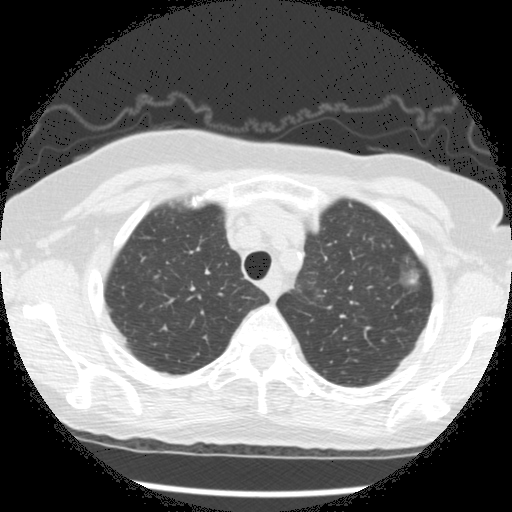
Axial slice from a low-dose chest CT screening exam. Second screening round (one year after baseline). Lung window (W 1500 / L -600 HU). 2.5 mm slice thickness. Slice 38 of 266 in the series. 512 × 512 image matrix, field of view 320 × 320 mm. Female participant, aged 73 years at enrolment. Former smoker at enrolment.
Expert-annotated lung lesion, bounding box <390,247,433,290> (left, top, right, bottom; pixels). The screening reader recorded 3 non-calcified nodules or masses ≥4 mm on this exam (left upper lobe, left upper lobe, left upper lobe); which of them this box marks is not recorded. Official screen result: positive, change unspecified: nodule(s) >= 4 mm or enlarging nodule(s), mass(es), or other non-specific abnormalities suspicious for lung cancer. Lung cancer was diagnosed 49 days after this screen: bronchiolo-alveolar adenocarcinoma, NOS, left upper lobe, well differentiated (G1), stage IA (AJCC 6th edition), 10 mm at pathology.